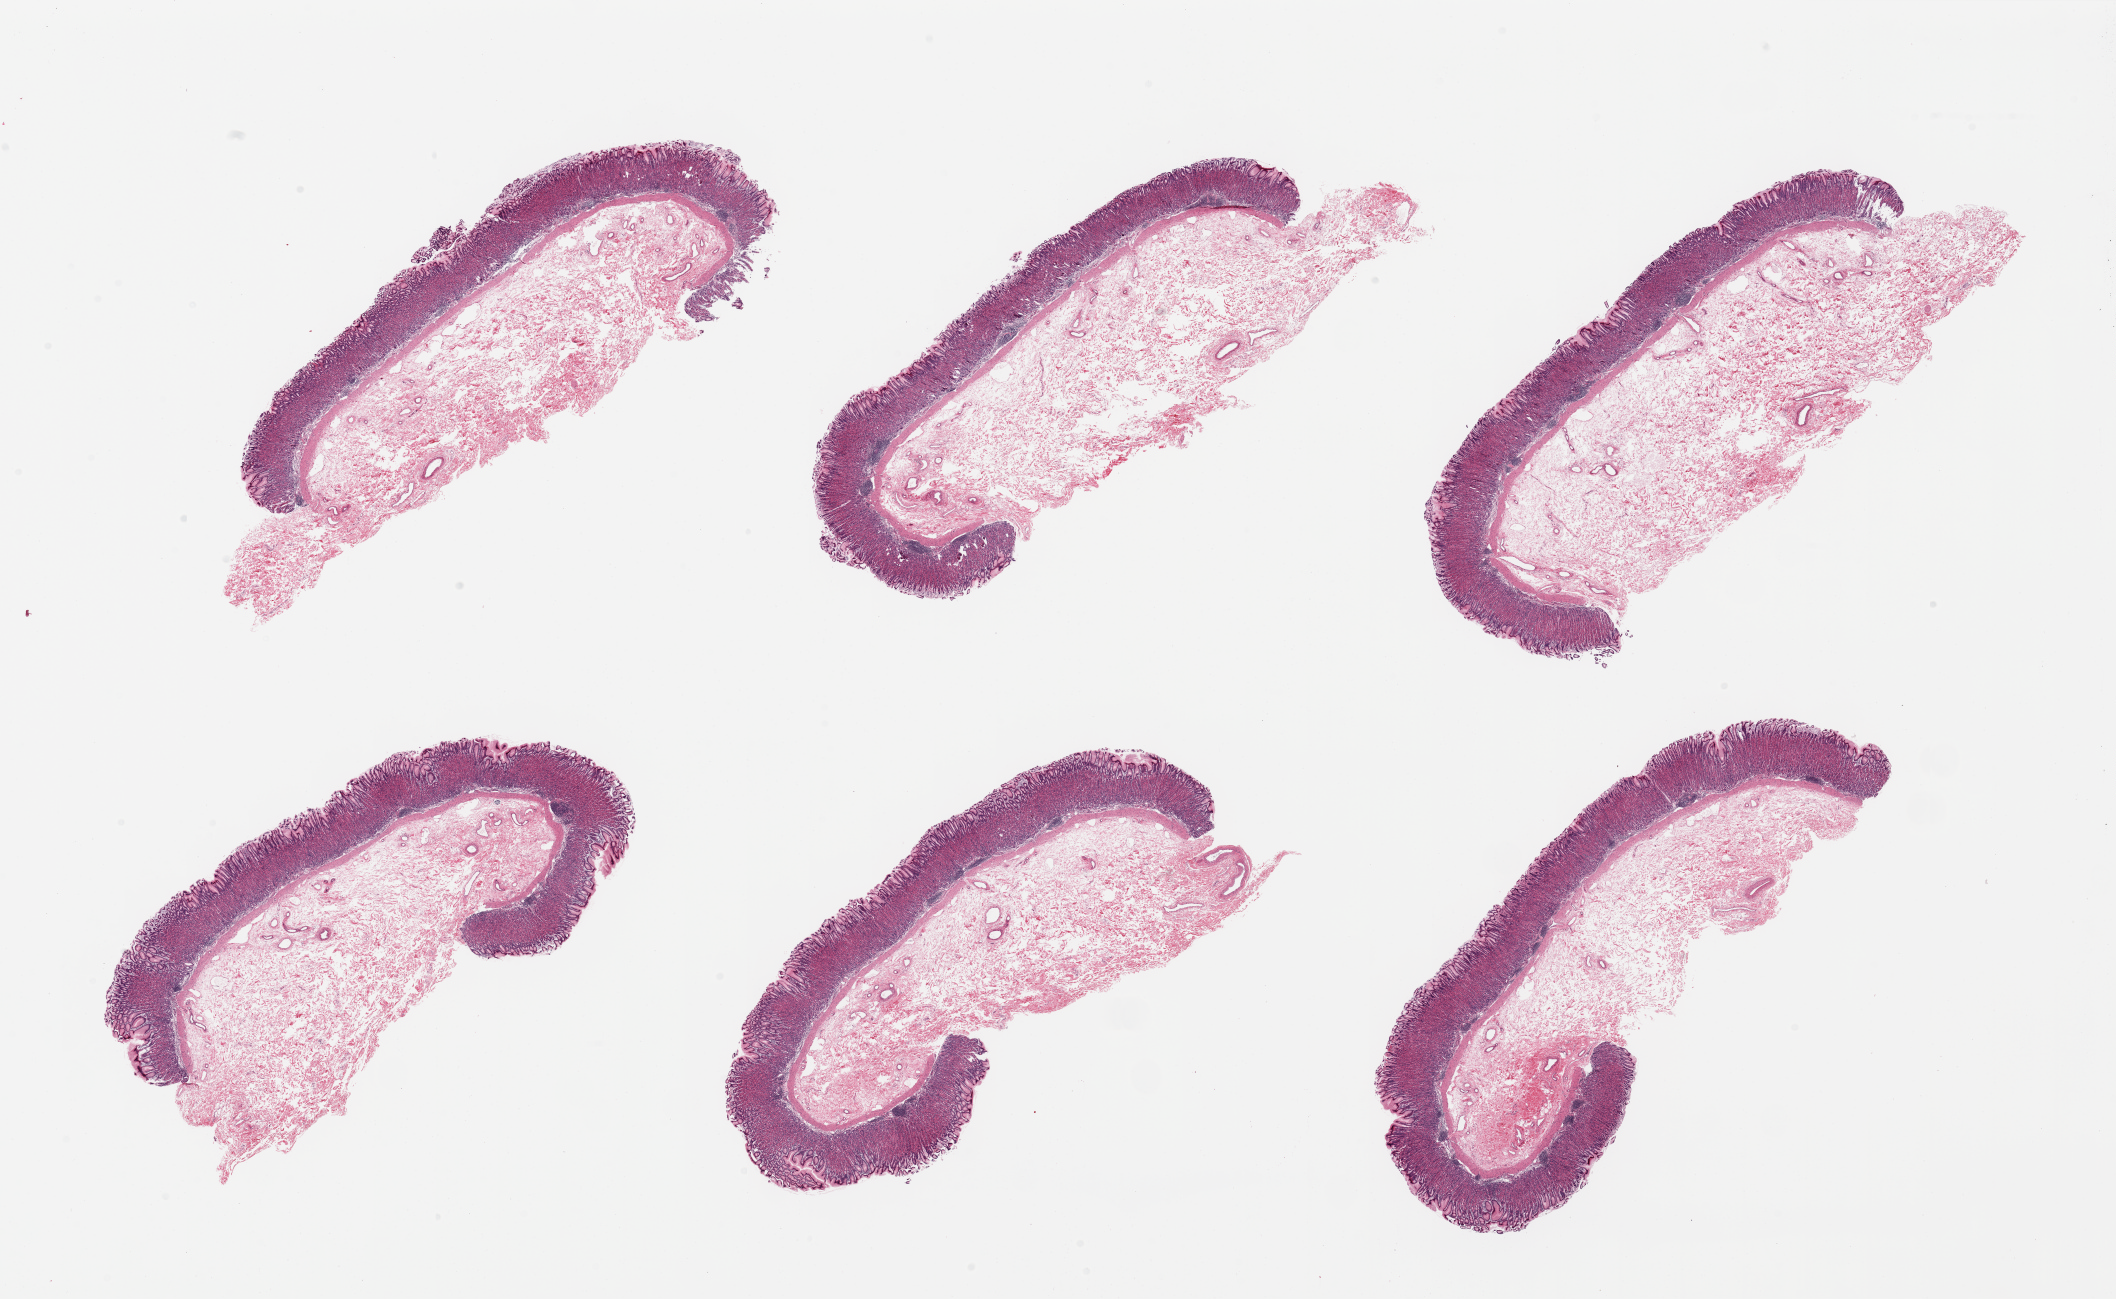
Digitized haematoxylin and eosin-stained section, shown as a low-resolution overview of the whole scanned area (about 33.5 x 20.5 mm); PAXgene-fixed paraffin-embedded (PFPE) section; section of stomach (target tissue); donor tissue sample. Donor sex: female.
Pathologist's review note for this sample: 6 pieces, mucosa well prserved, up to ~1mm, 20-25% thickness.